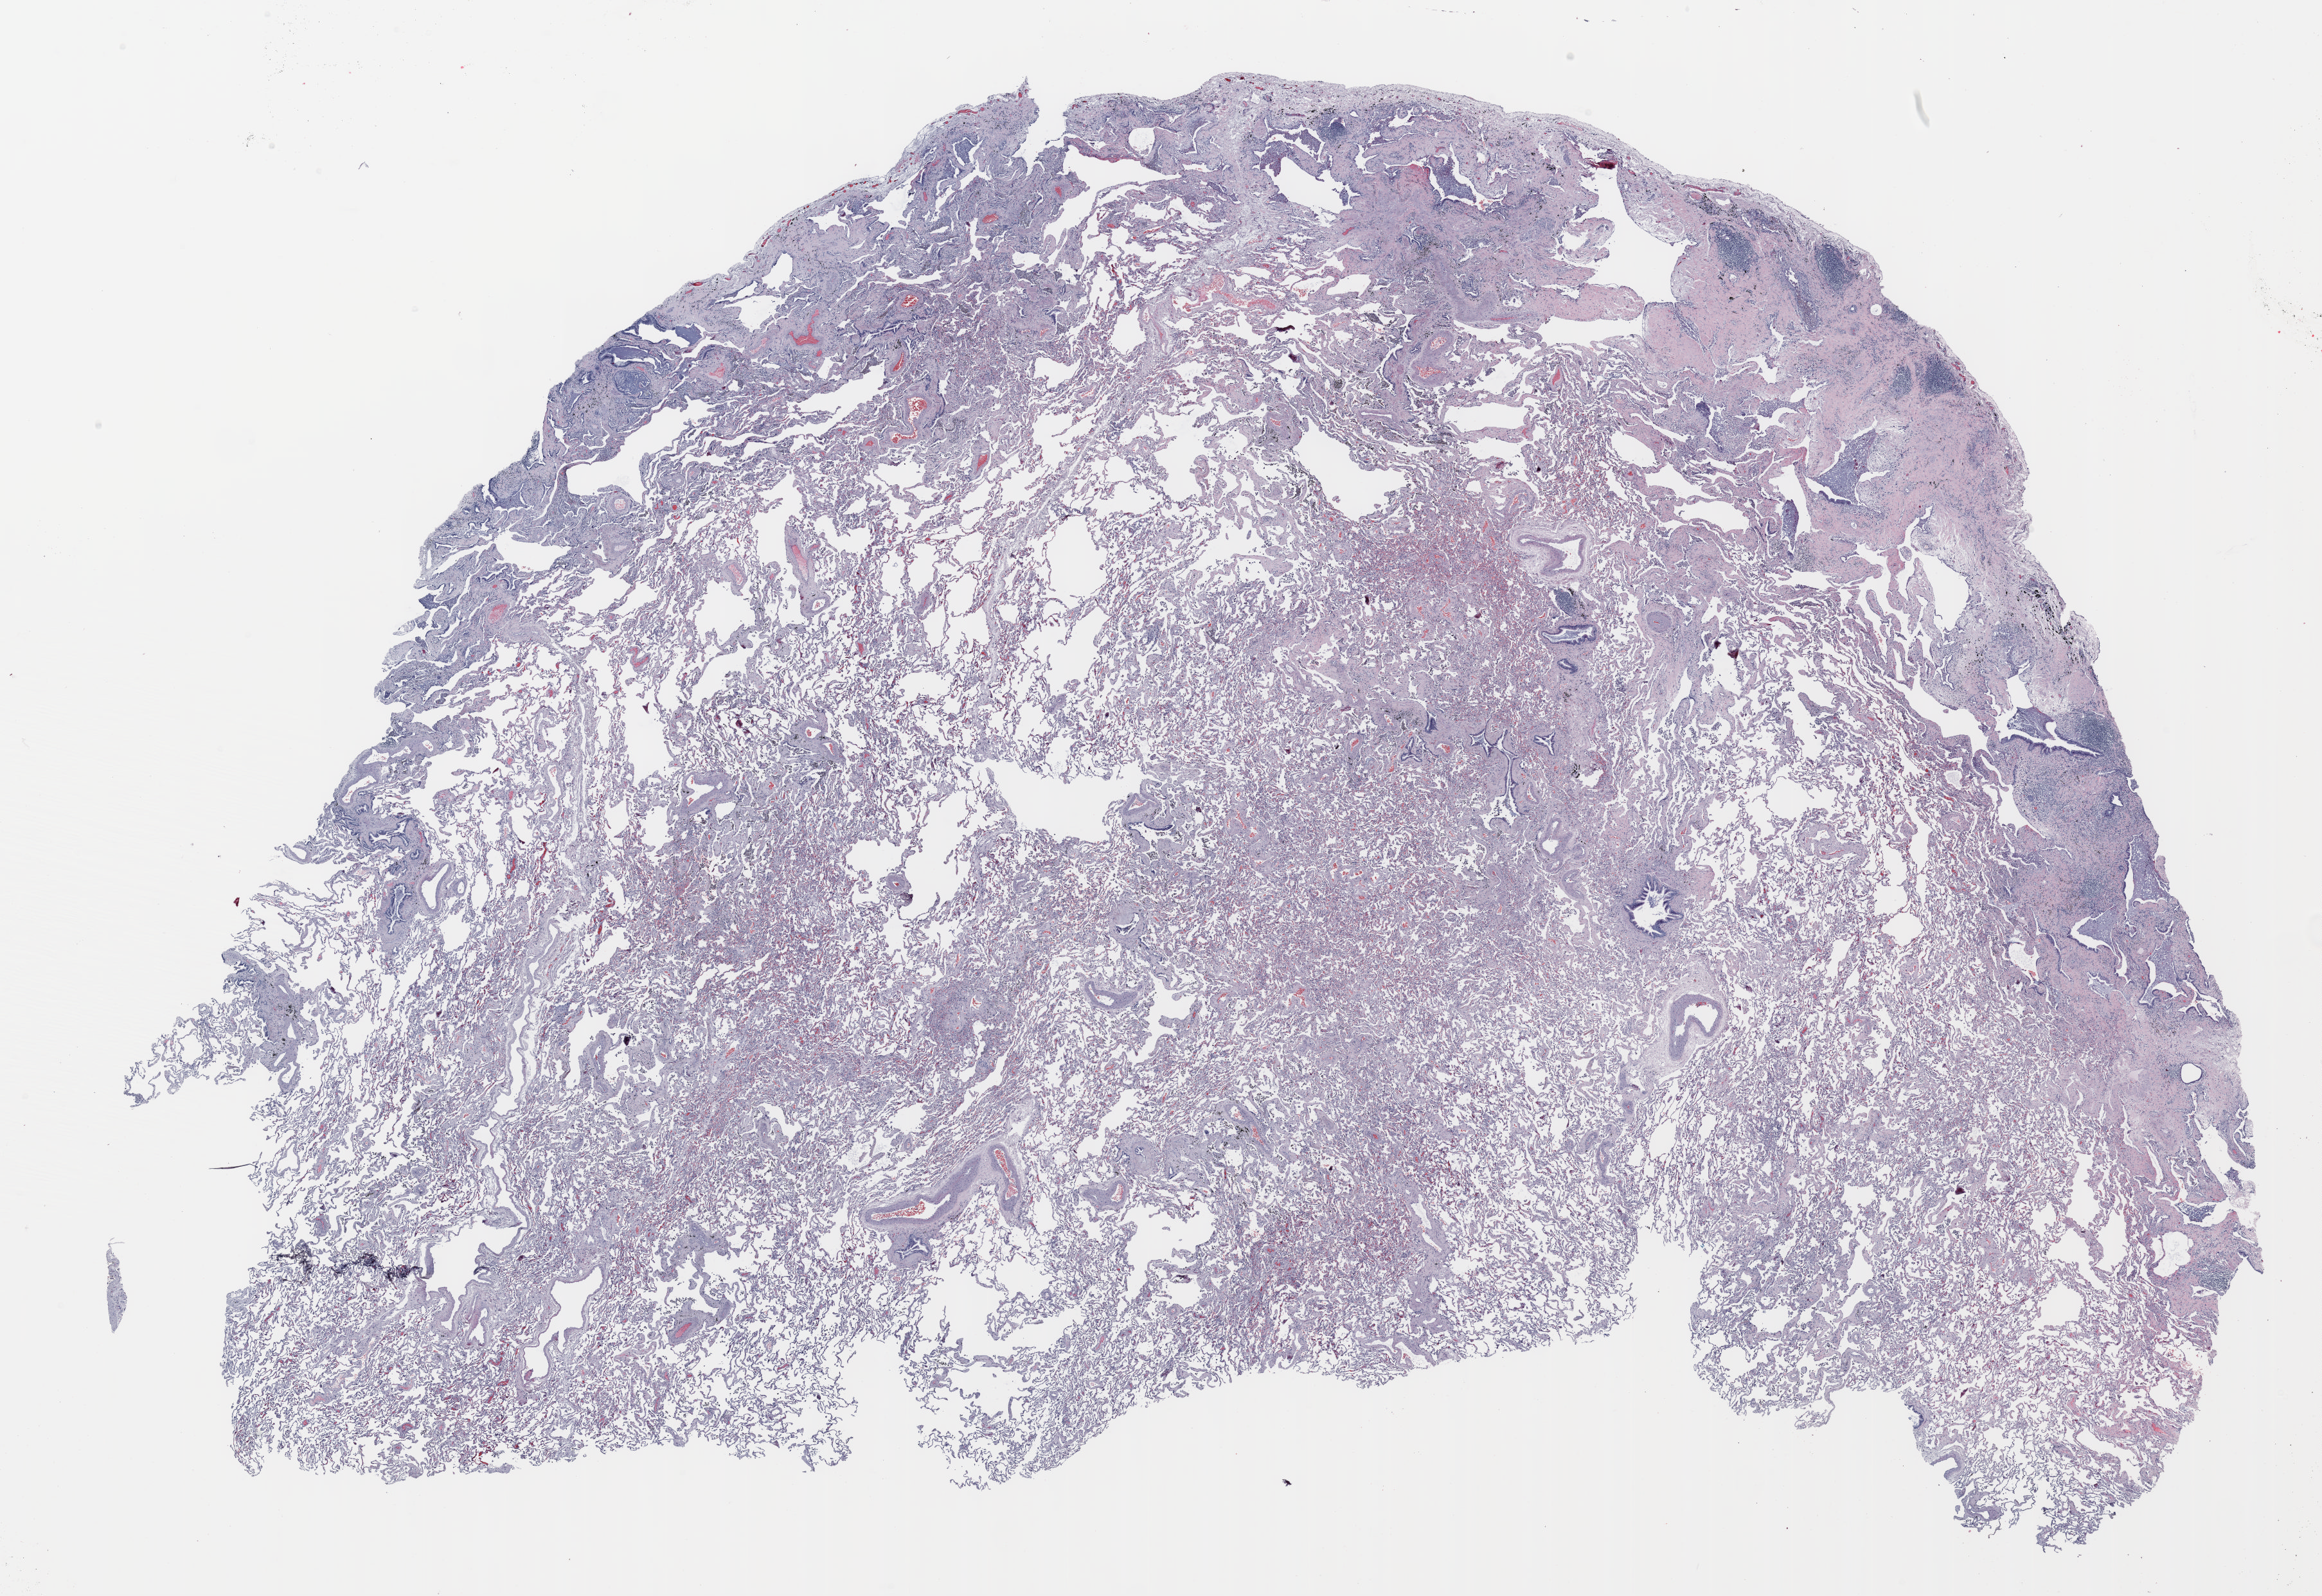
Whole-slide histology image, H&E-stained — a low-resolution overview of the entire scanned area, about 29.0 x 20.0 mm (from a 20x scan); formalin-fixed paraffin-embedded (FFPE) section; lung. Male, age 71 at enrolment. Current smoker at enrolment. Grade: poorly differentiated (G3).
Stage (AJCC 6th edition): IA. Participant's lung-cancer diagnosis: Squamous cell carcinoma, NOS. Primary tumour location (clinical record): right upper lobe. Tumour size (pathology): 30 mm.